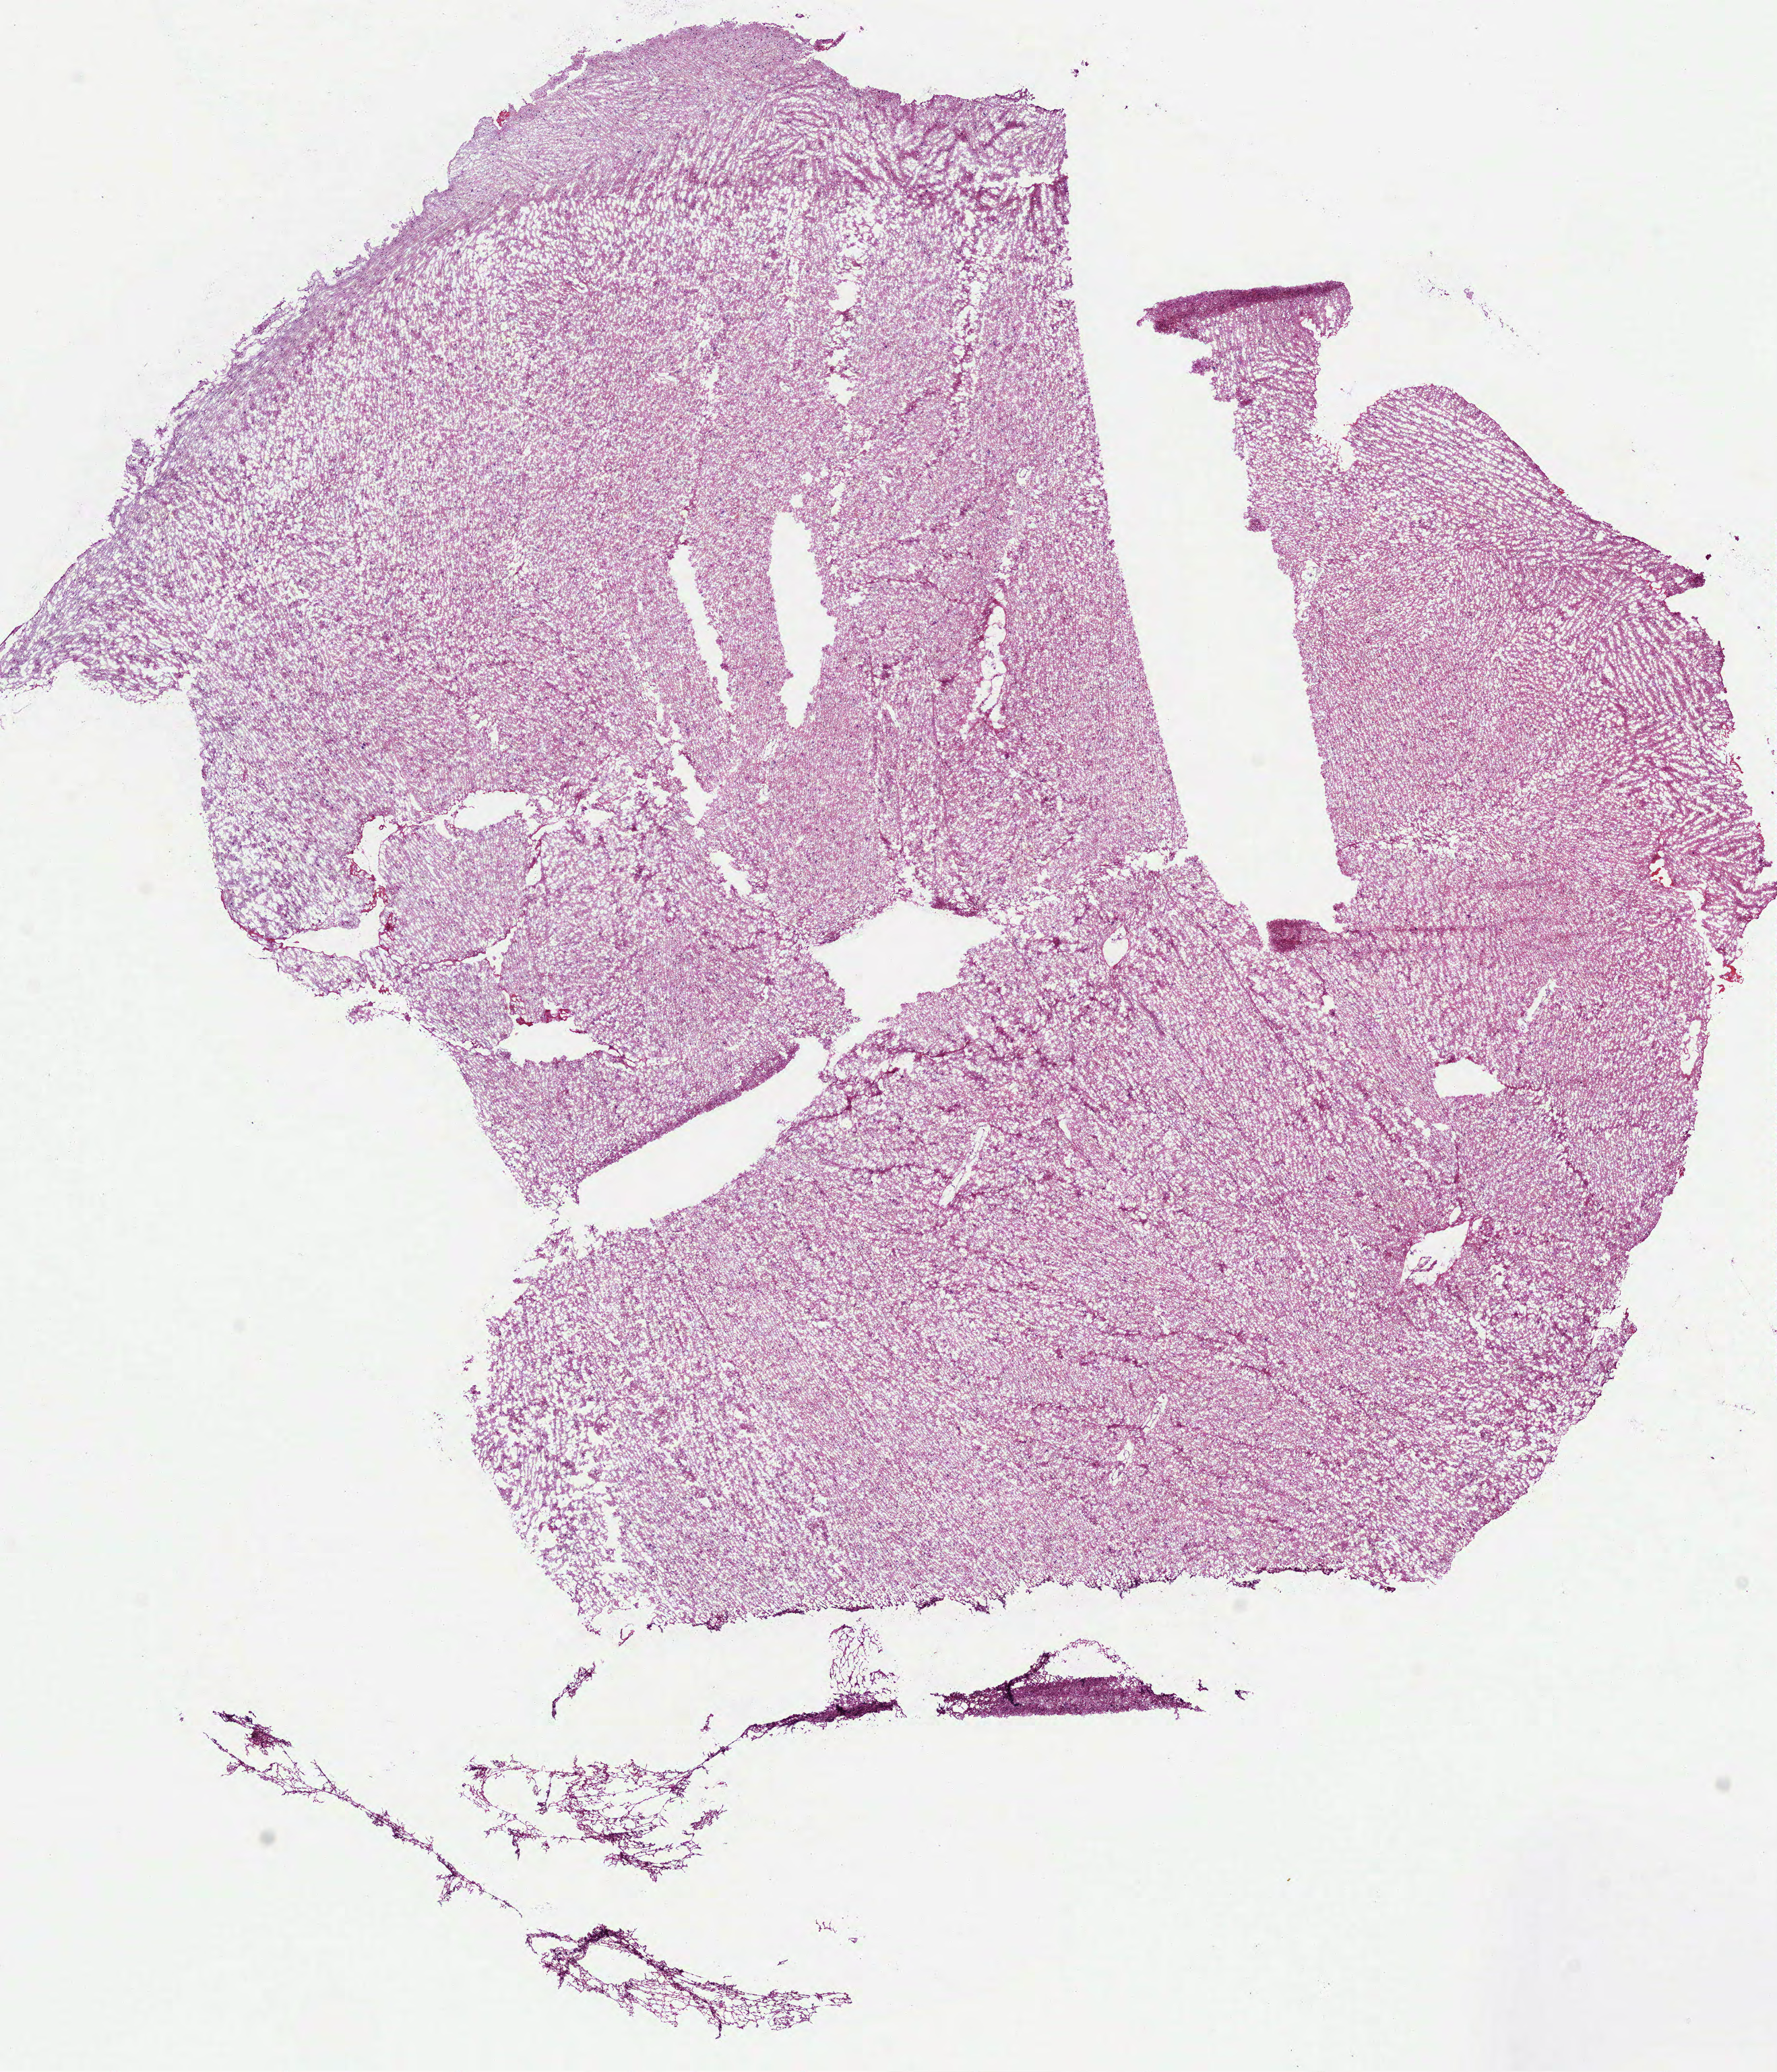
Whole-slide histology image, H&E-stained — low-resolution overview of the scanned area, about 10.6 x 12.4 mm (from a 40x scan), frozen section, primary tumour sample from the brain. Patient: male, age at initial diagnosis 44 years. Histologic grade: G3 (poorly differentiated). Pathologist review of this section (percent, as recorded): tumour cells 100%, tumour nuclei 50%, normal cells 0%, stromal cells 0%, necrosis 0%.
- diagnosis: Astrocytoma, anaplastic